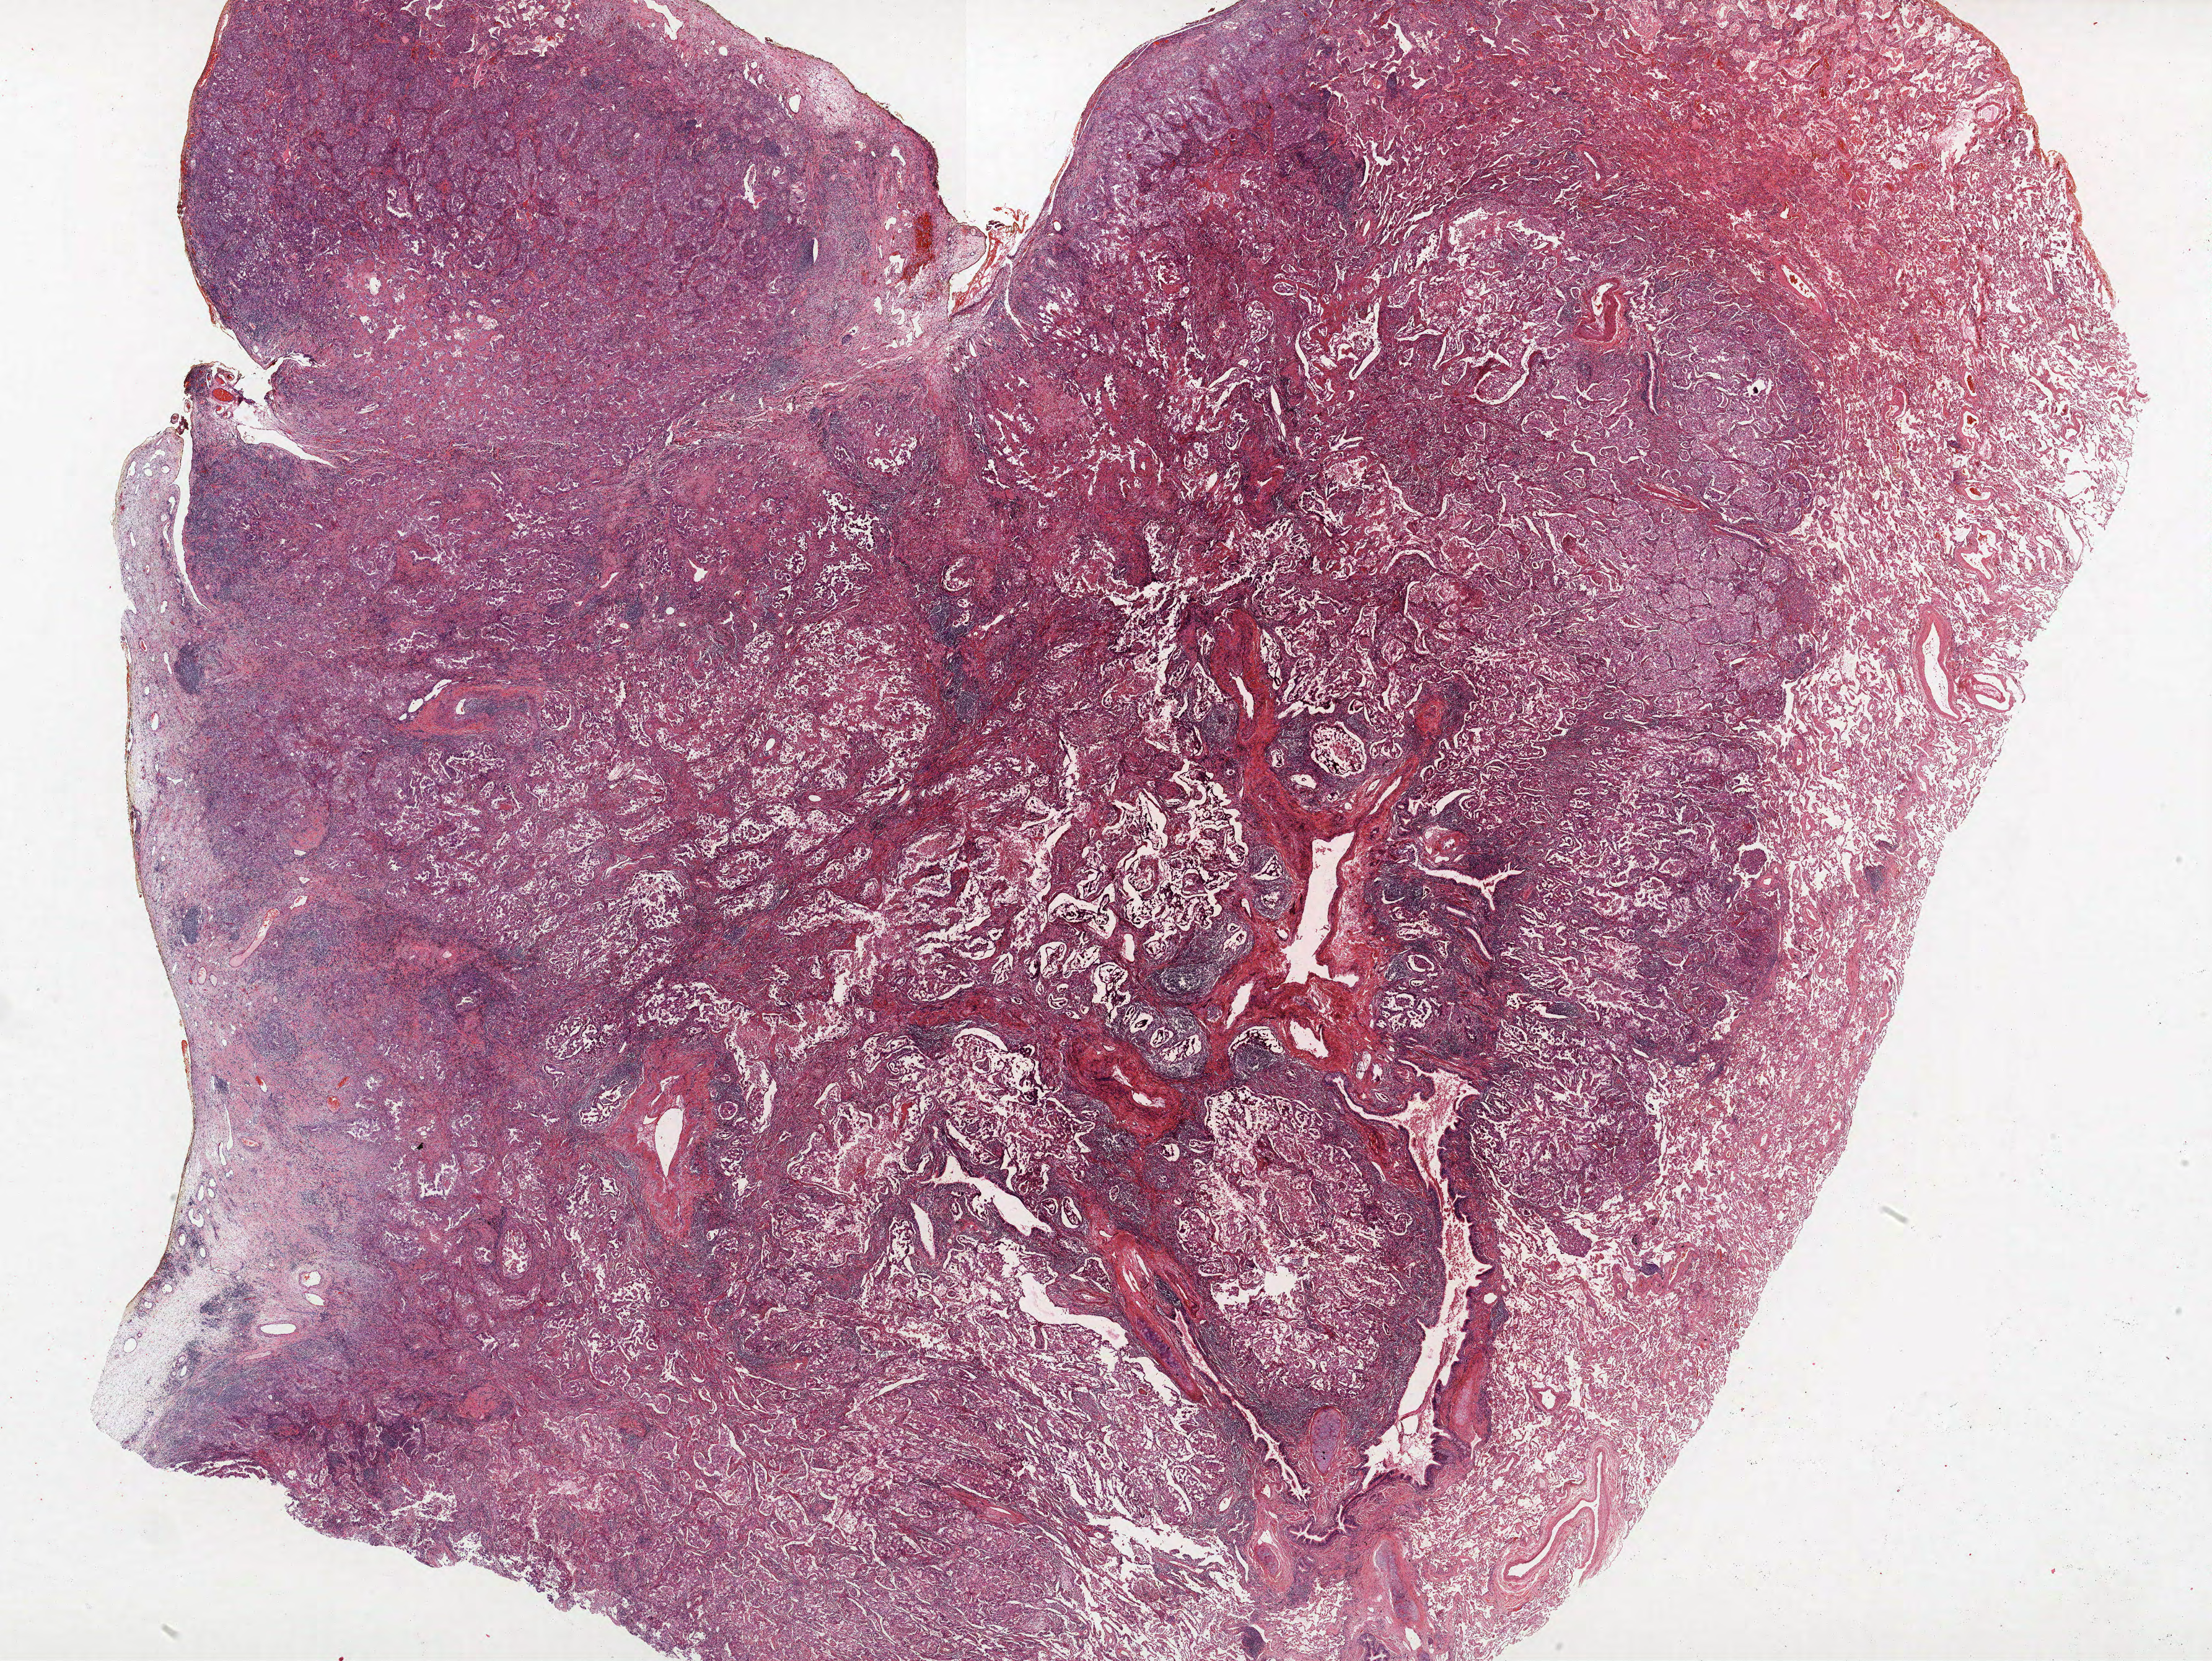
Hematoxylin and eosin (H&E) stained whole-slide image, low-resolution overview of the scanned area, about 28.6 x 21.4 mm (acquisition: 40x scan), formalin-fixed paraffin-embedded (FFPE) section, lung tissue. Female patient, aged 58 at enrolment. Former smoker at enrolment. Grade: poorly differentiated (G3).
* primary tumour location (clinical record): left upper lobe
* tumour size (pathology): 37 mm
* participant's lung-cancer diagnosis: Acinar cell carcinoma
* stage (AJCC 6th edition): IIIA